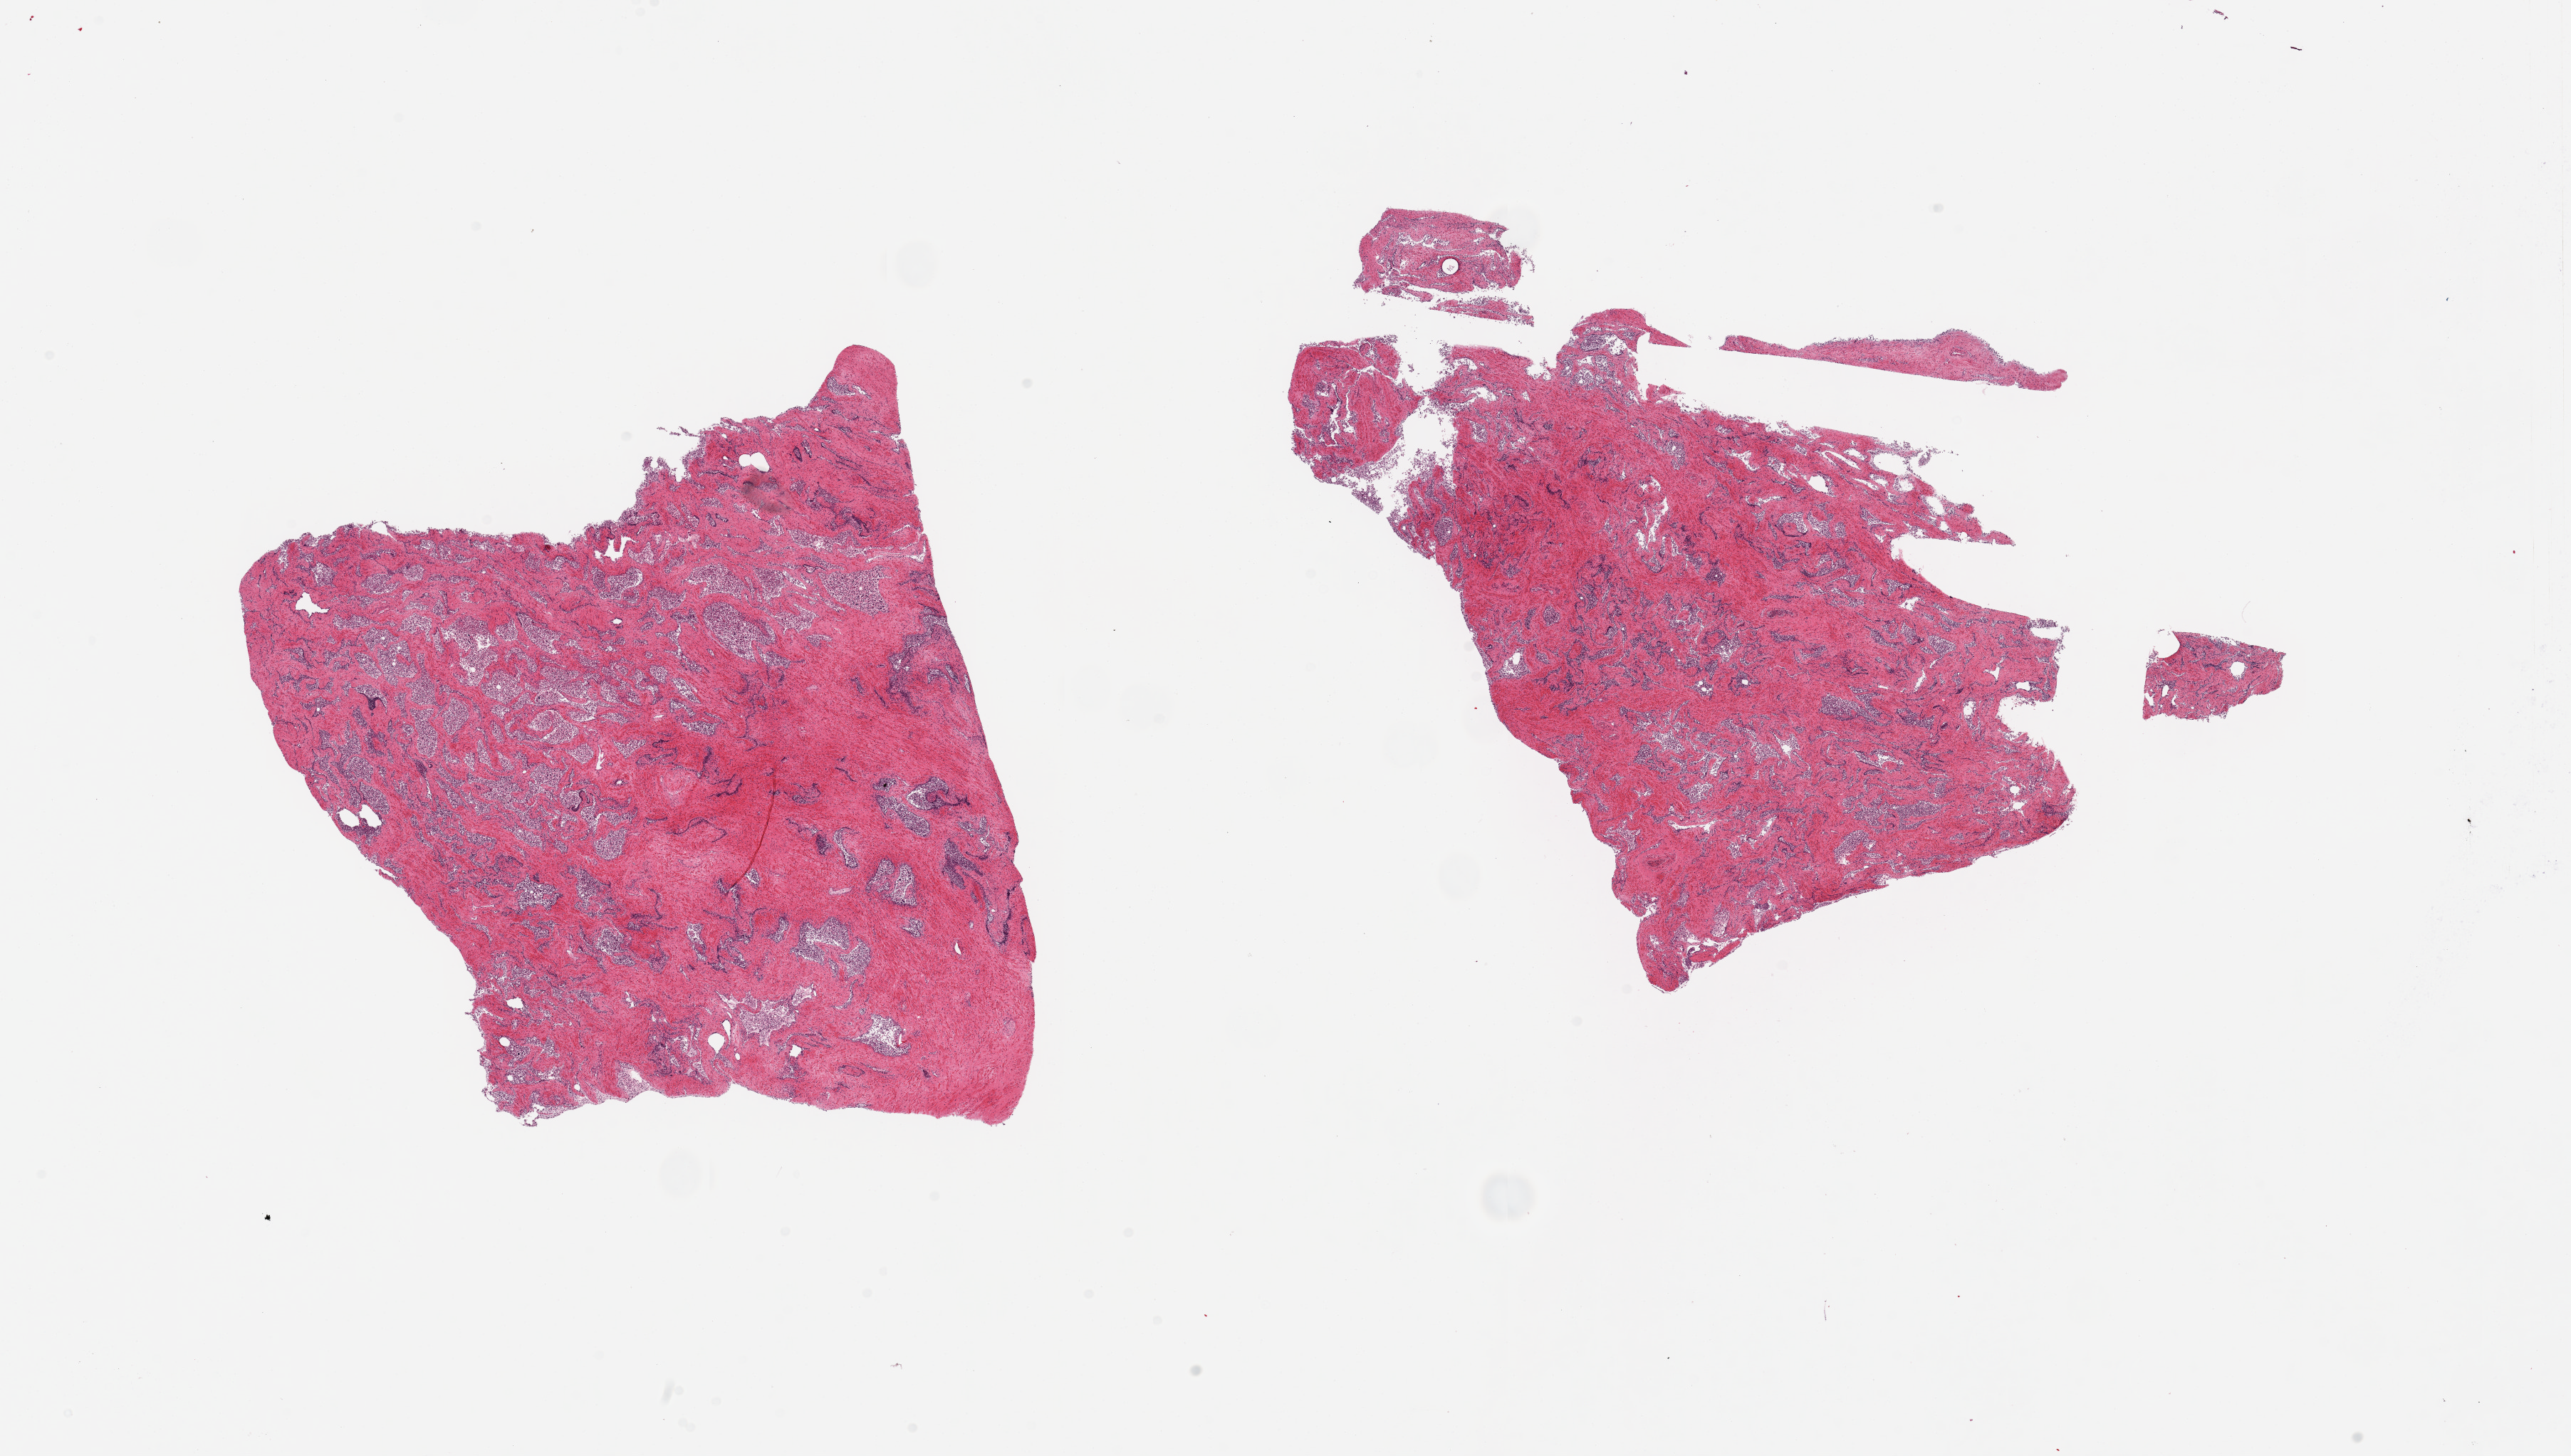
Digitized hematoxylin and eosin (H&E)-stained section — low-resolution overview of the scanned area, about 28.5 x 16.2 mm. PAXgene-fixed, paraffin-embedded tissue. Sampled site (target tissue): prostate. Tissue donor sample. Donor sex: male.
* pathologist's review note for this sample: 2 pieces; fibromuscular stroma and autolysed glands with sloughing of glandular epithelium